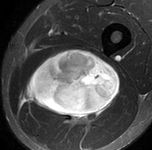
MRI of an extremity soft-tissue mass, one axial slice; slice 64 of 90 in the series (ordered by position); STIR; MR volume resampled by the dataset authors to the PET/CT grid (not the native acquisition matrix); 3.27 mm slice thickness; 152 × 150 image matrix, field of view 148 × 146 mm. Male patient. From the clinical record (not read from this slice): histological type: undifferentiated pleomorphic liposarcoma; grade: high; site of the primary tumour: left thigh.
Structures marked on this image (expert contour drawn on MRI and transferred to this co-registered scan by the dataset authors):
- gross tumour volume including surrounding oedema: bounding box (x1, y1, x2, y2) in pixels: (22, 48, 120, 127)
- gross tumour volume (mass): (23, 48, 120, 120)